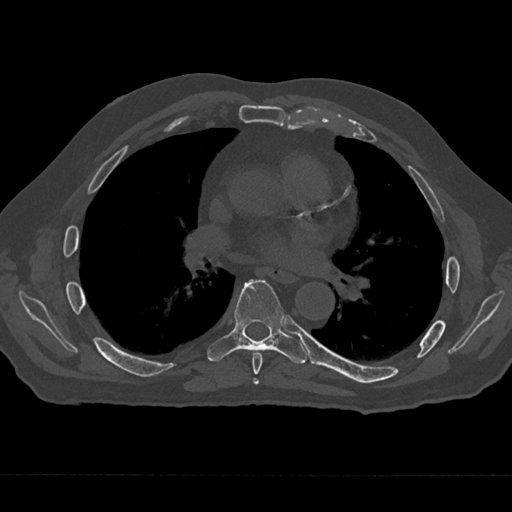
CT including the spine, one axial slice; slice 384 of 797 in the series (ordered by position); bone window (W 1800 / L 400 HU); 0.5 mm slice thickness; 512 × 512 image matrix. Patient: male, 75 years. From the clinical record (not read from this slice): primary cancer: renal; vertebrae with lytic lesions (as recorded): T4.
Outlined on this slice (semi-automatic segmentation, software-assisted and operator-edited):
- T6 vertebra: bounding box [x1, y1, x2, y2] px = [252, 352, 263, 385]
- T7 vertebra: [207, 280, 307, 364]